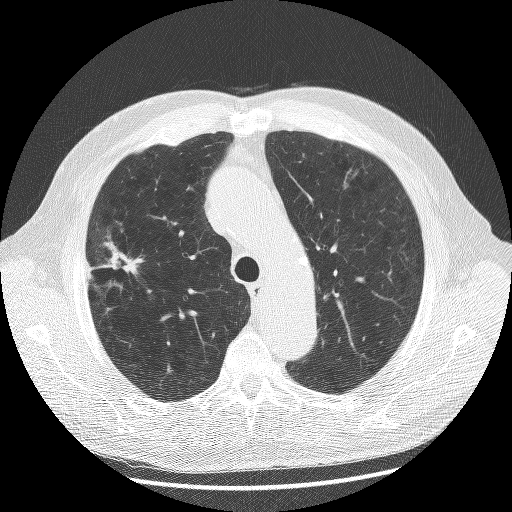
Chest CT (low-dose screening protocol), one axial image. Baseline annual screen. Lung window (W 1500 / L -600 HU). 2.5 mm slice thickness. 512 × 512 image matrix, field of view 380 × 380 mm. Male, age 70 years at enrolment.
Expert reader's lesion annotation, bounding box [x1, y1, x2, y2] px = [78, 233, 146, 306]. The screening reader recorded 2 non-calcified nodules or masses ≥4 mm on this exam; which of them this box marks is not recorded. Lung cancer was diagnosed 23 days after this screen: non-small cell carcinoma, right upper lobe, poorly differentiated (G3), stage IA (AJCC 6th edition), 20 mm at pathology.